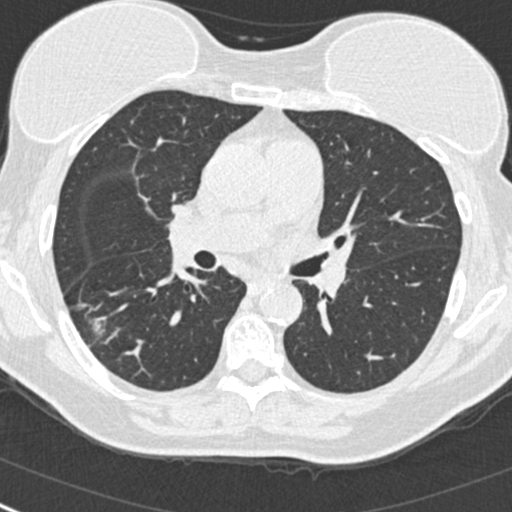
Low-dose screening chest CT, one axial slice. Slice 152 of 268 in the series (ordered by position). Reconstruction kernel B30f. 120 kVp. Lung window (W 1500 / L -600 HU). 1 mm slice thickness. 512 × 512 image matrix, field of view 296 × 296 mm.
Annotated regions visible in this slice (manually delineated by an expert):
- lesion 1 (tumor, upper lobe of right lung): box from (x=93, y=322) to (x=104, y=335) px